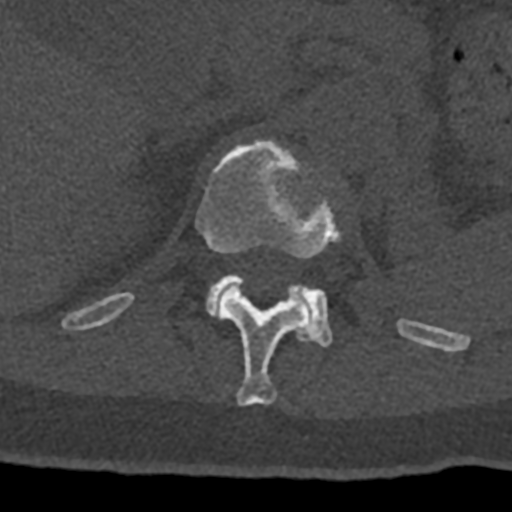
CT including the spine, one axial slice; slice 475 of 797 in the series (ordered by position); reconstruction kernel Br40s/3; 120 kVp; bone window (W 1800 / L 400 HU); 0.5 mm slice thickness; 512 × 512 image matrix, field of view 160 × 160 mm. Patient: male, 74 years. Case-level facts recorded for this patient, not image findings: primary cancer: renal.
Structures marked on this image (semi-automatically segmented with operator editing):
- L1 vertebra: bounding box <206,274,332,347> (left, top, right, bottom; pixels)
- T12 vertebra: <70,139,432,405>